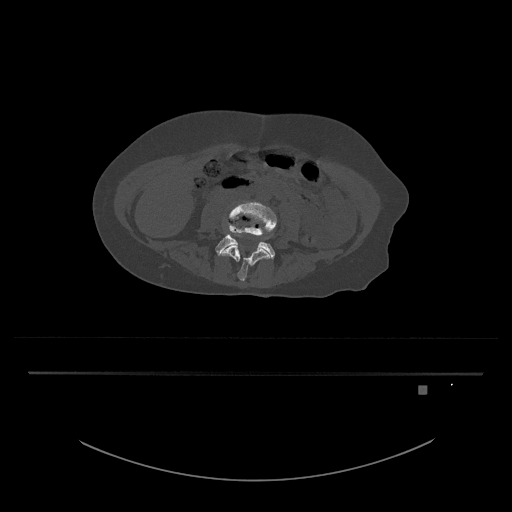
CT including the spine, one axial slice; position 337 of 797 along the scan axis; 120 kVp; bone window (W 1800 / L 400 HU); 0.5 mm slice thickness; 512 × 512 image matrix, field of view 500 × 500 mm. Female patient, age 57 years. From the clinical record (not read from this slice): primary cancer: cervical.
Annotated regions visible in this slice (semi-automatically segmented with operator editing):
- L4 vertebra: bounding box [x1, y1, x2, y2] px = [220, 201, 277, 281]